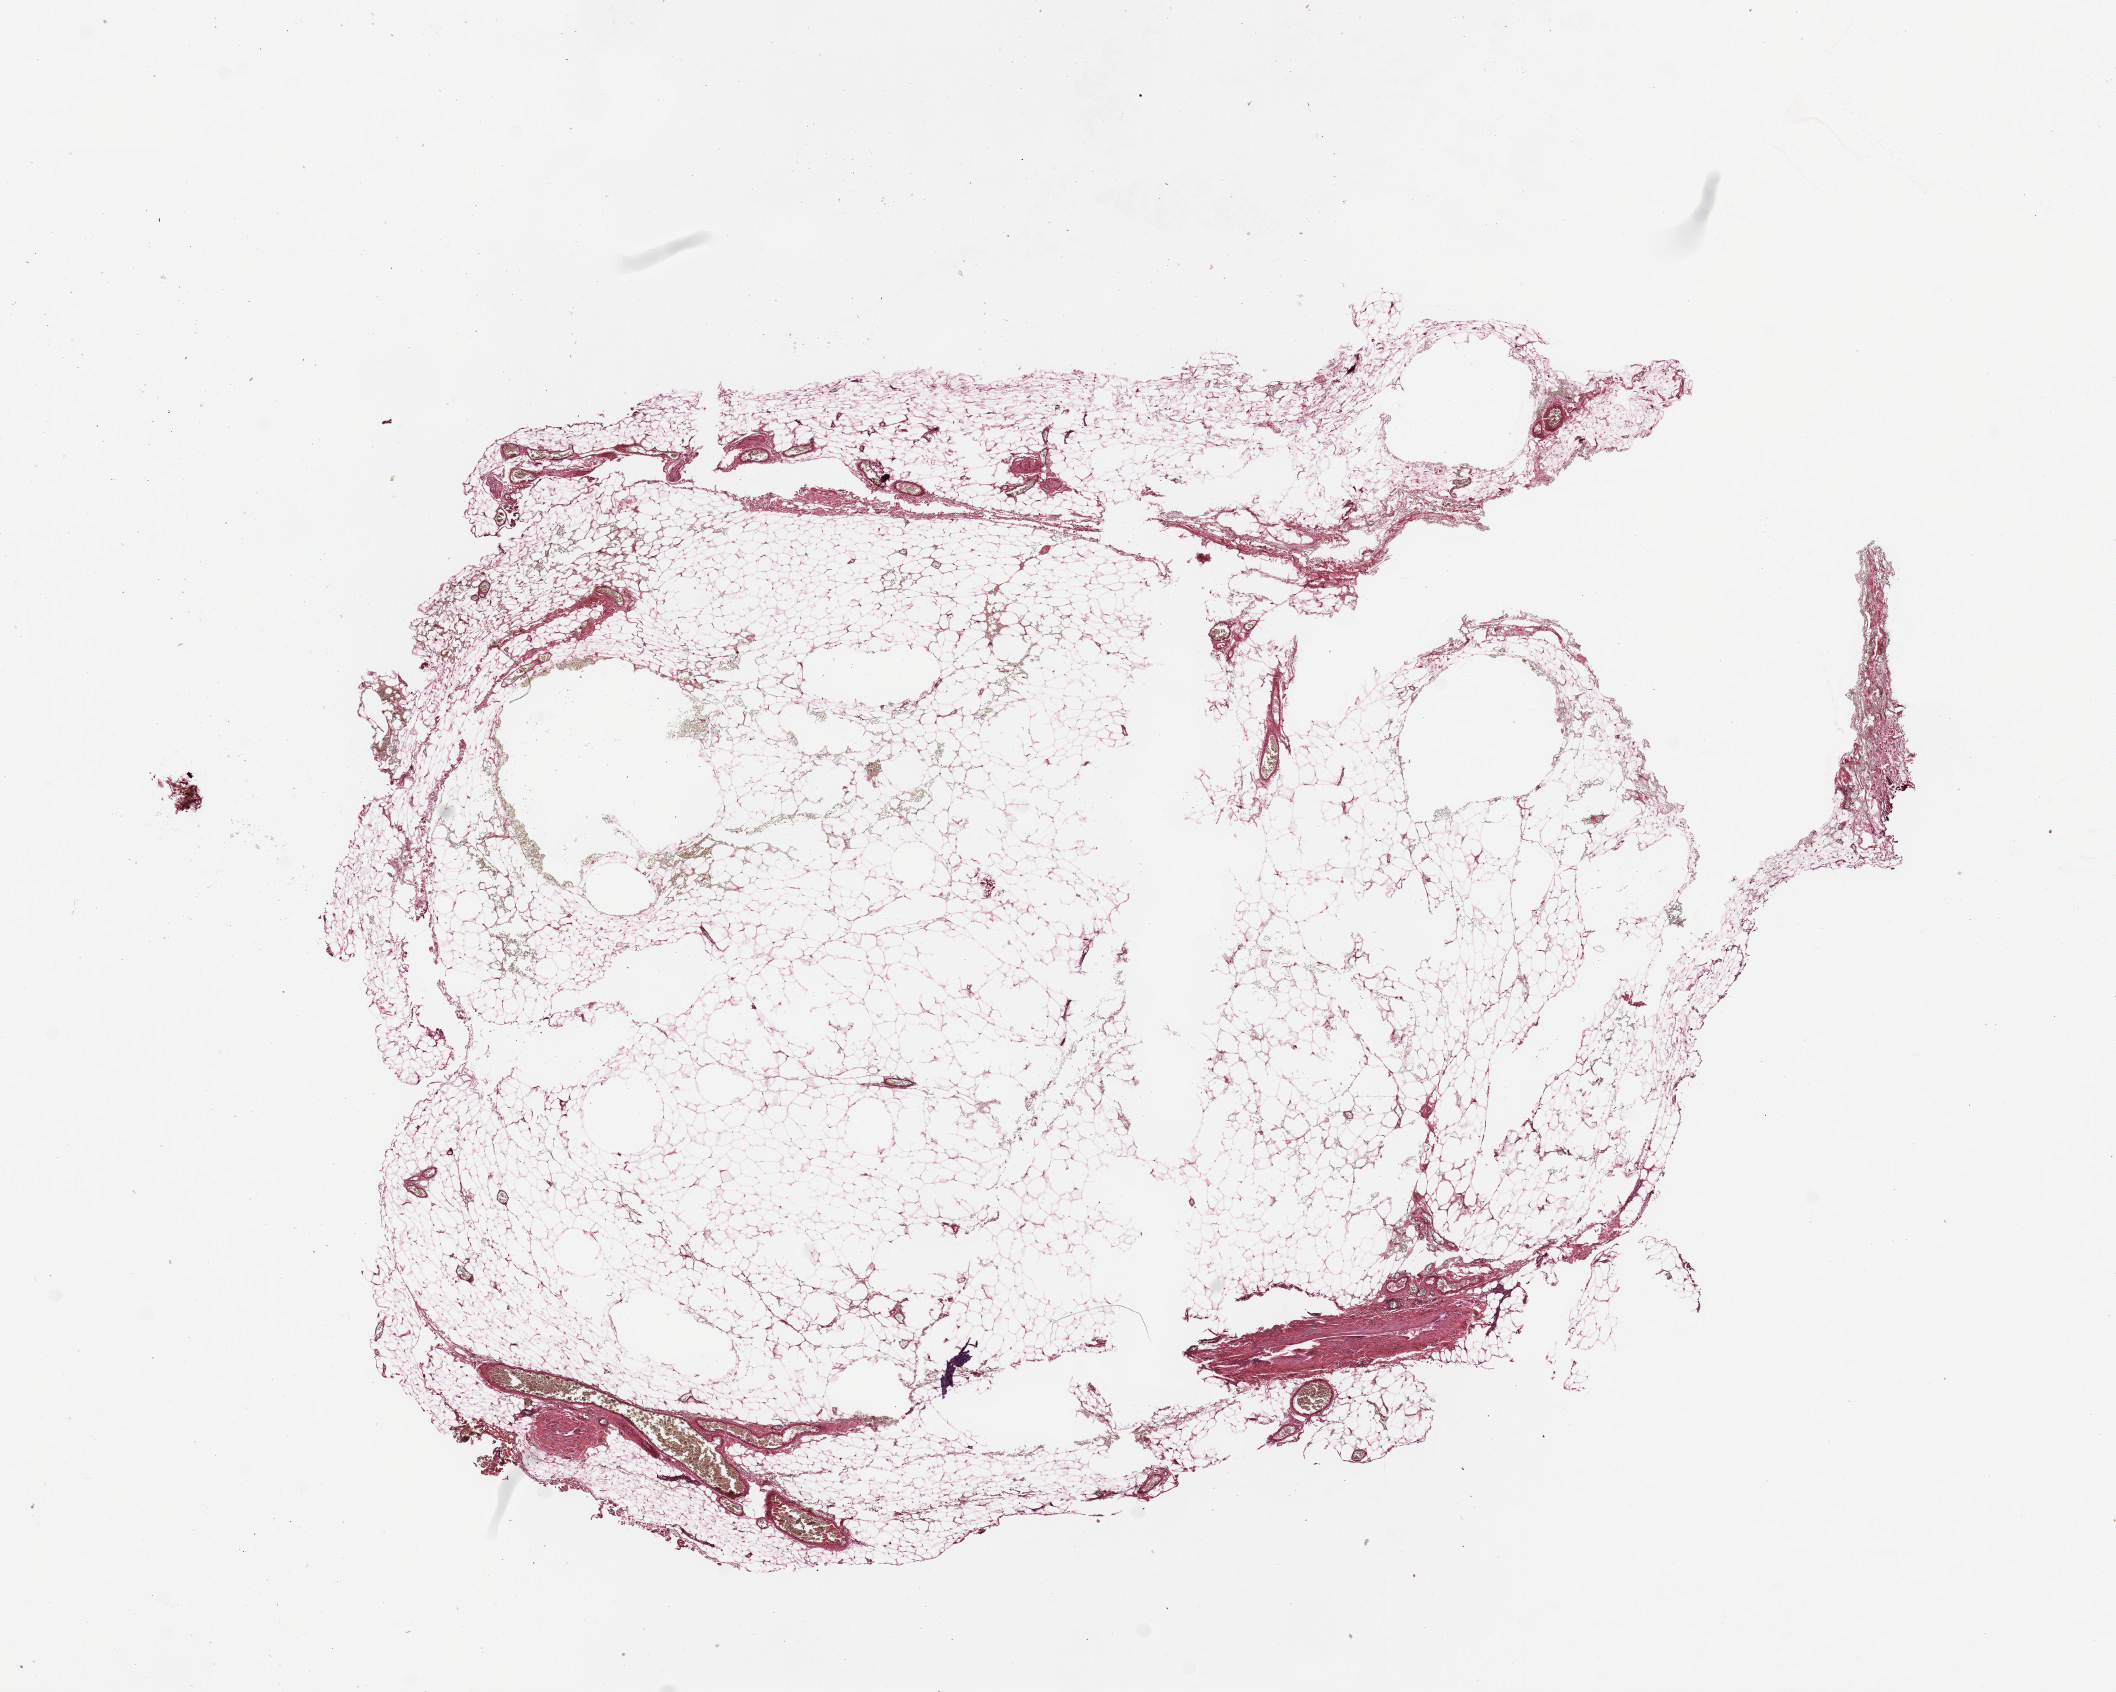
H&E-stained whole-slide image, low-resolution overview of the scanned area, about 16.7 x 13.4 mm; normal (non-tumour) tissue (melanoma cohort); sampled site not recorded. 60-year-old male patient.
This section: normal (non-tumour) tissue from the same patient. Patient diagnosis (cohort enrolment): cutaneous melanoma (skin).